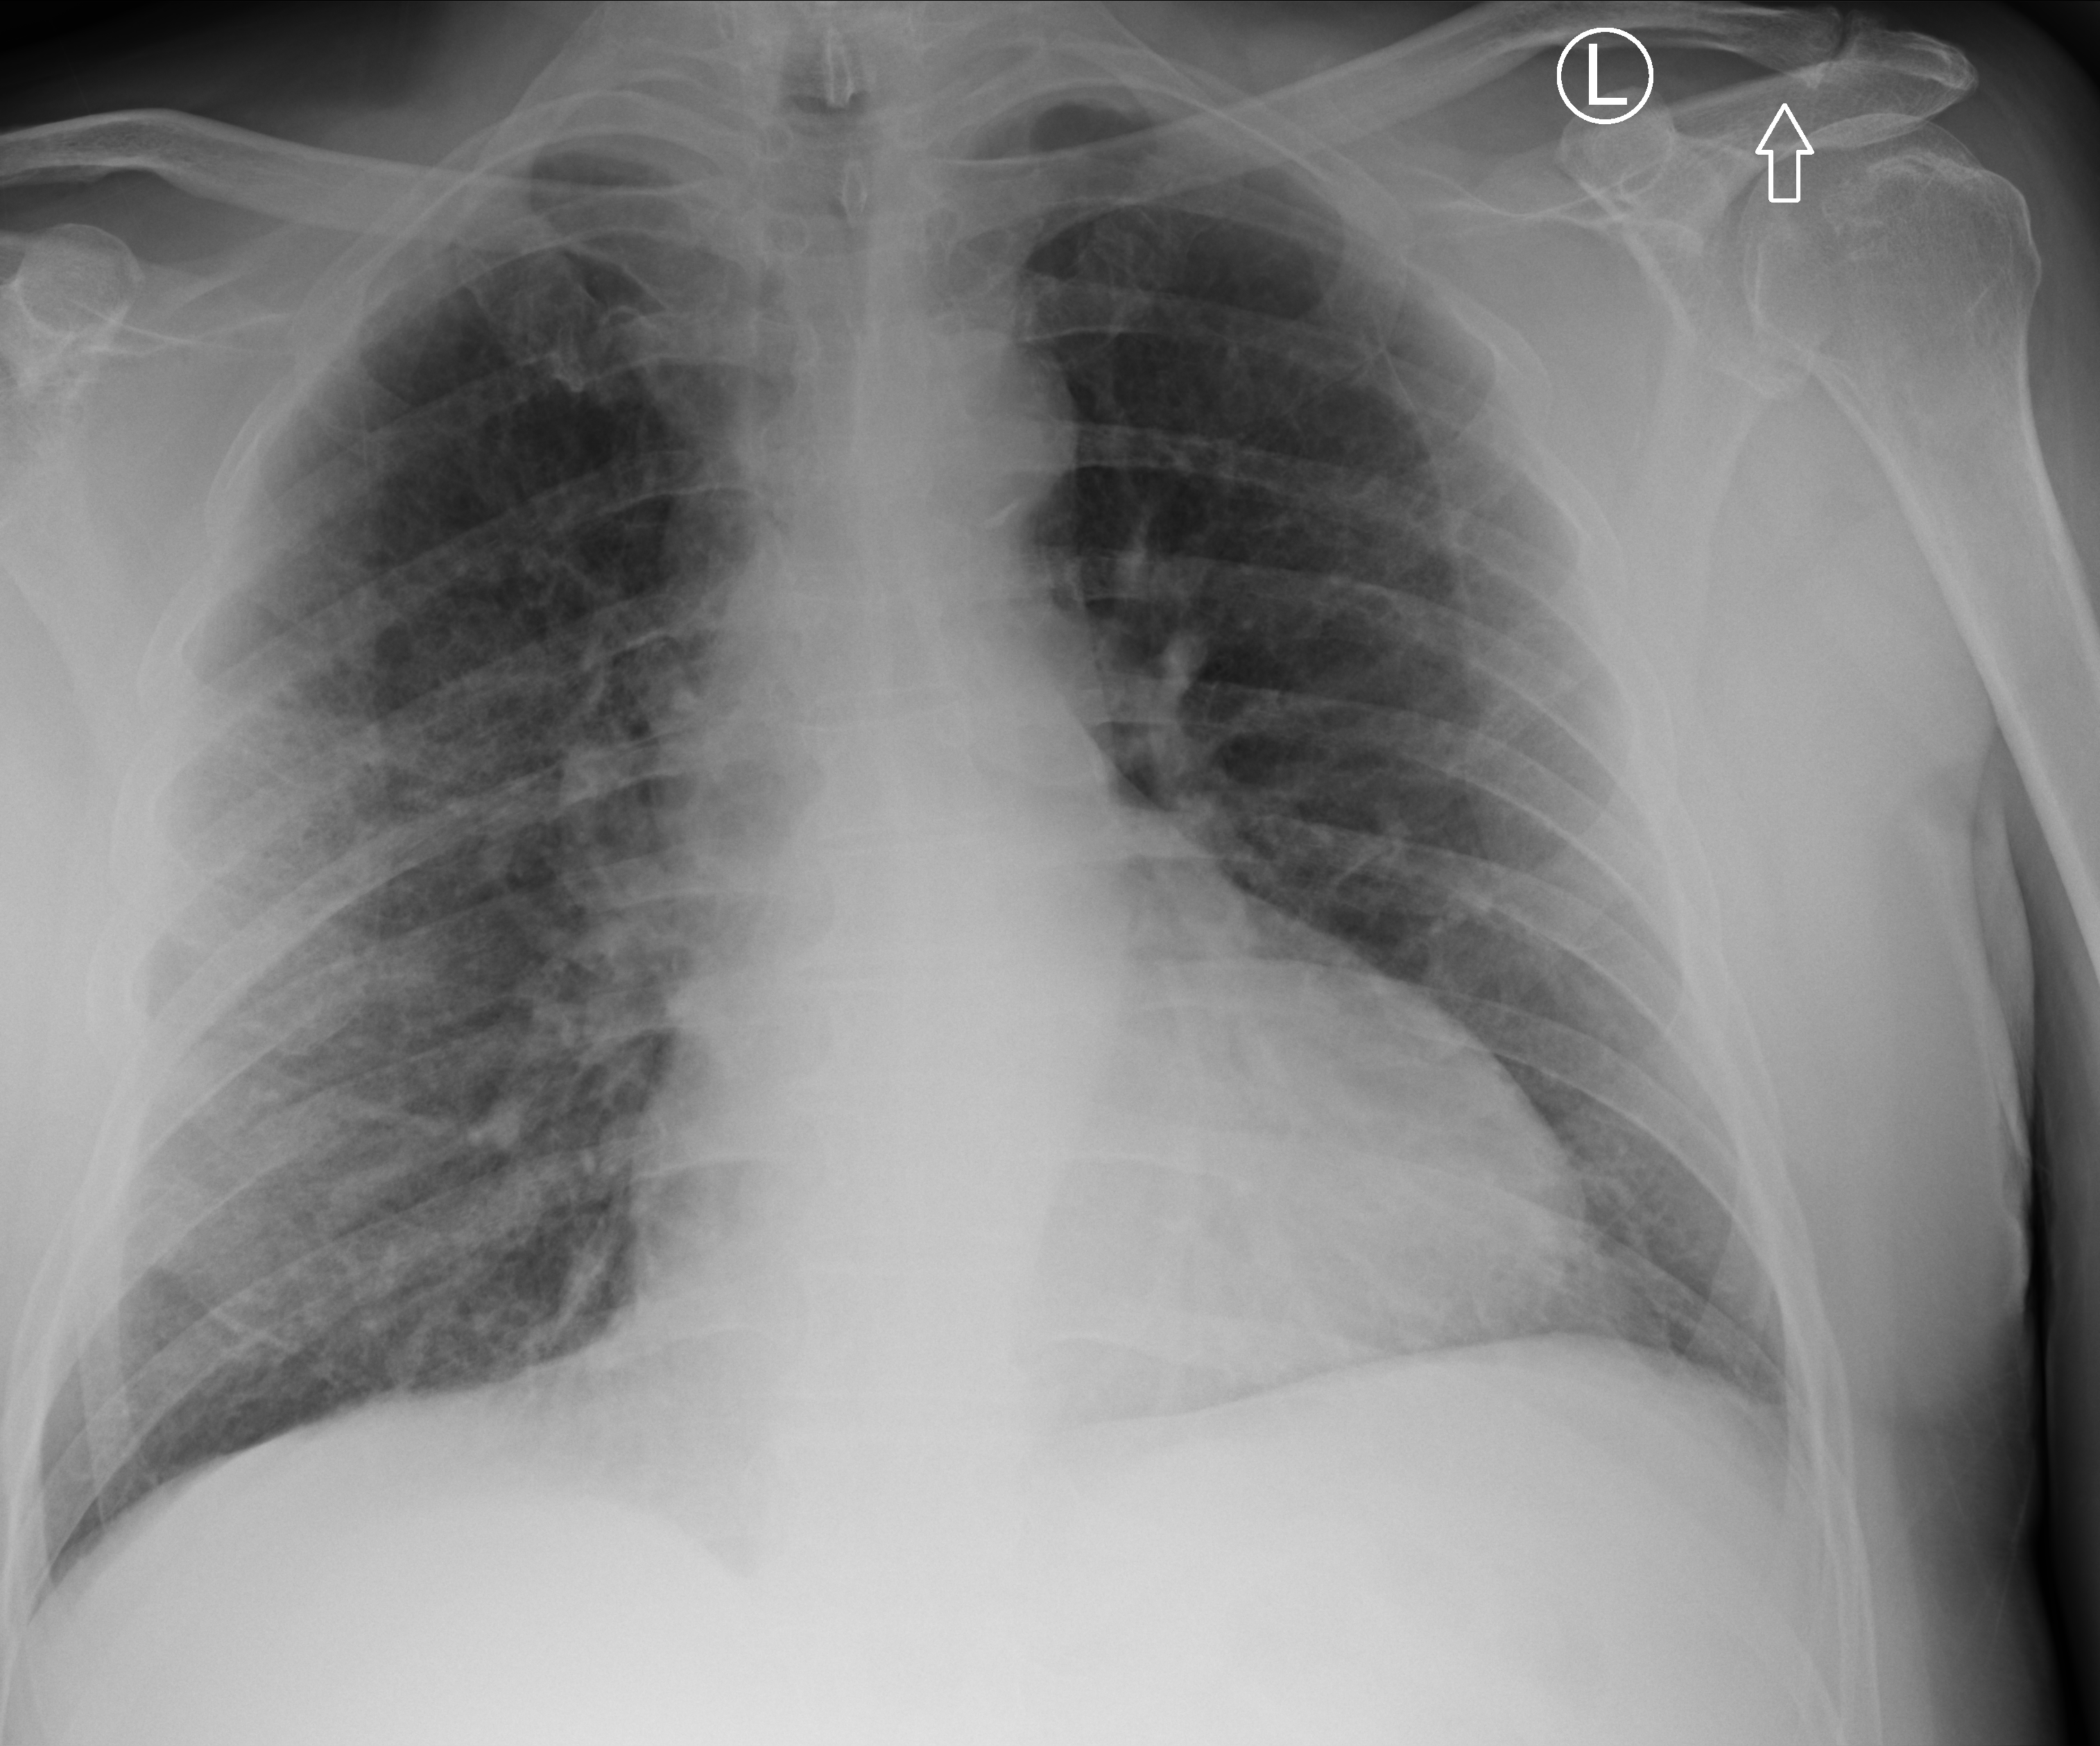
Chest X-ray (portable), anteroposterior (AP) projection. Male patient hospitalised with COVID-19, age 60–74 years.
From the hospital-stay record, not from the radiograph (when in the stay this image was taken is not recorded): admitted to intensive care during this hospital stay: no; smoking status (admission record): former; mechanically ventilated during this hospital stay: no.